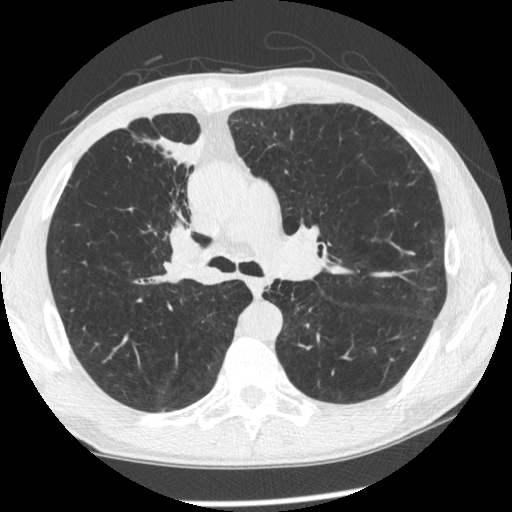
Low-dose screening chest CT, one axial slice; slice 146 of 261 in the series (ordered by position); reconstruction kernel STANDARD; lung window (W 1500 / L -600 HU); 1.25 mm slice thickness; 512 × 512 image matrix.
Annotated regions visible in this slice (expert manual segmentation):
- lesion 1 (tumor, upper lobe of right lung): bounding box <149,134,206,236> (left, top, right, bottom; pixels)